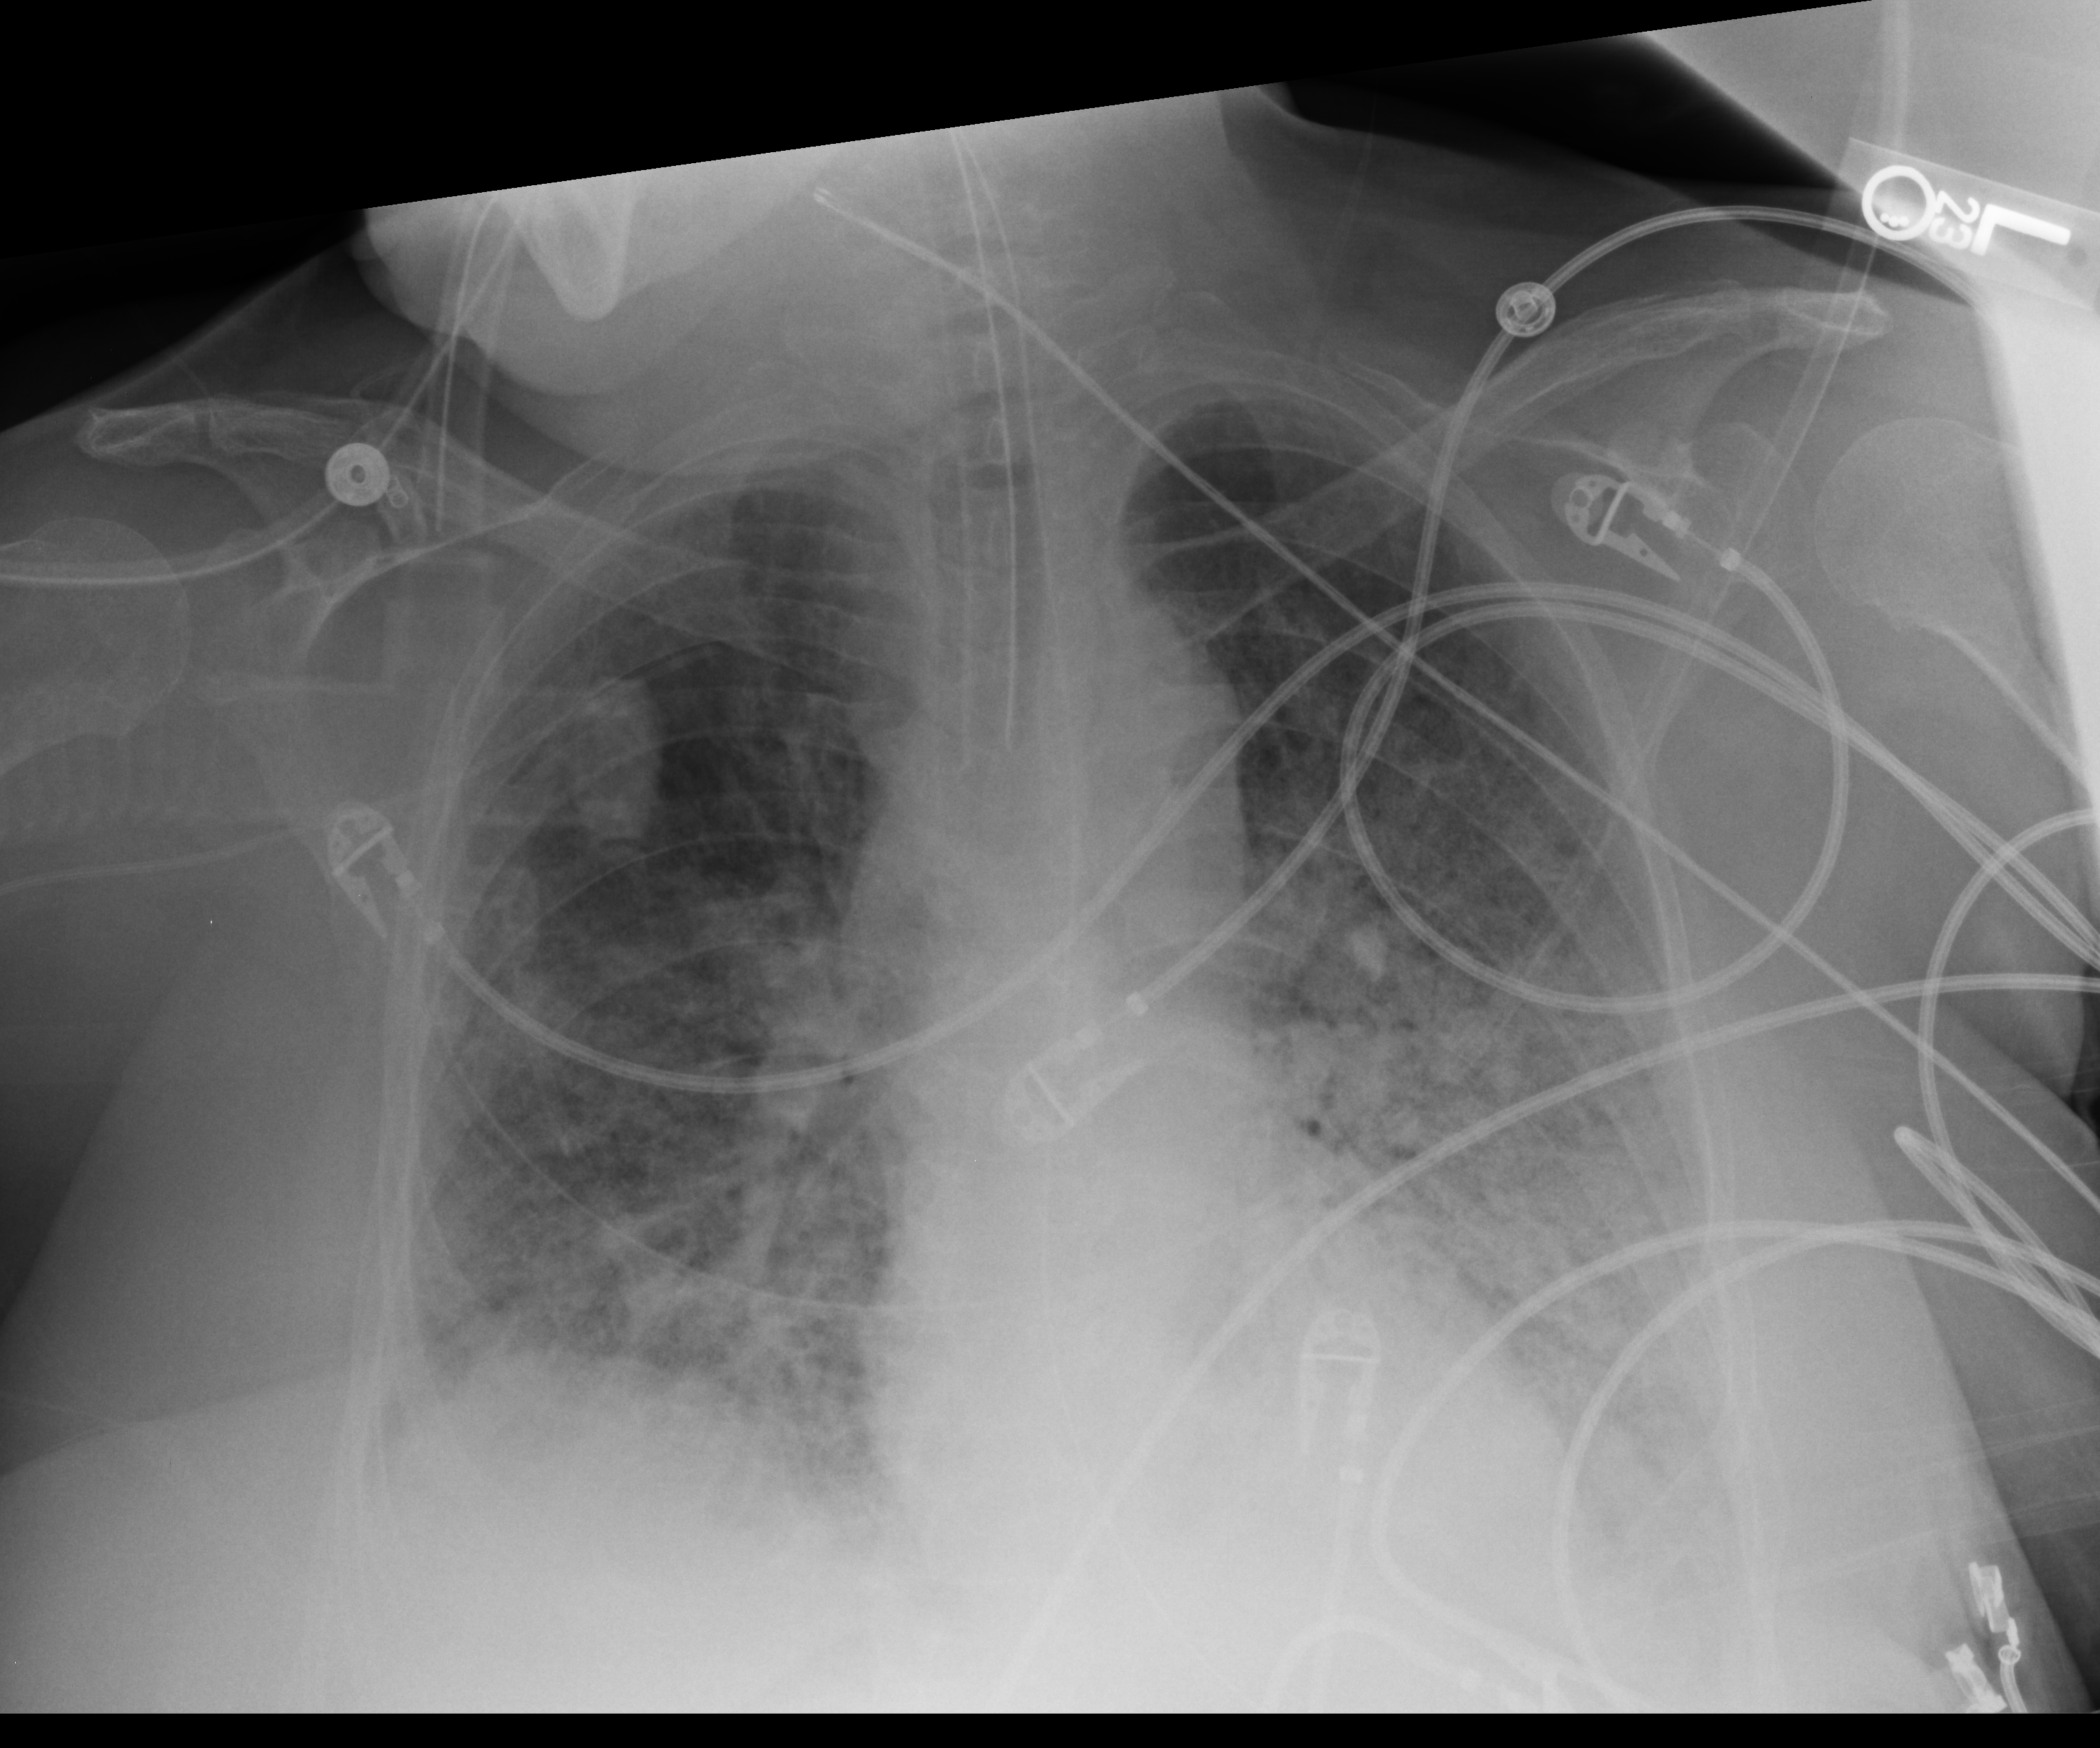
Portable chest radiograph; anteroposterior (AP) projection. Patient hospitalised with COVID-19; female, aged 60–74 years.
From the hospital-stay record, not from the radiograph (when in the stay this image was taken is not recorded):
- chronic kidney disease (admission record): no
- mechanically ventilated during this hospital stay: yes
- COPD (admission record): no